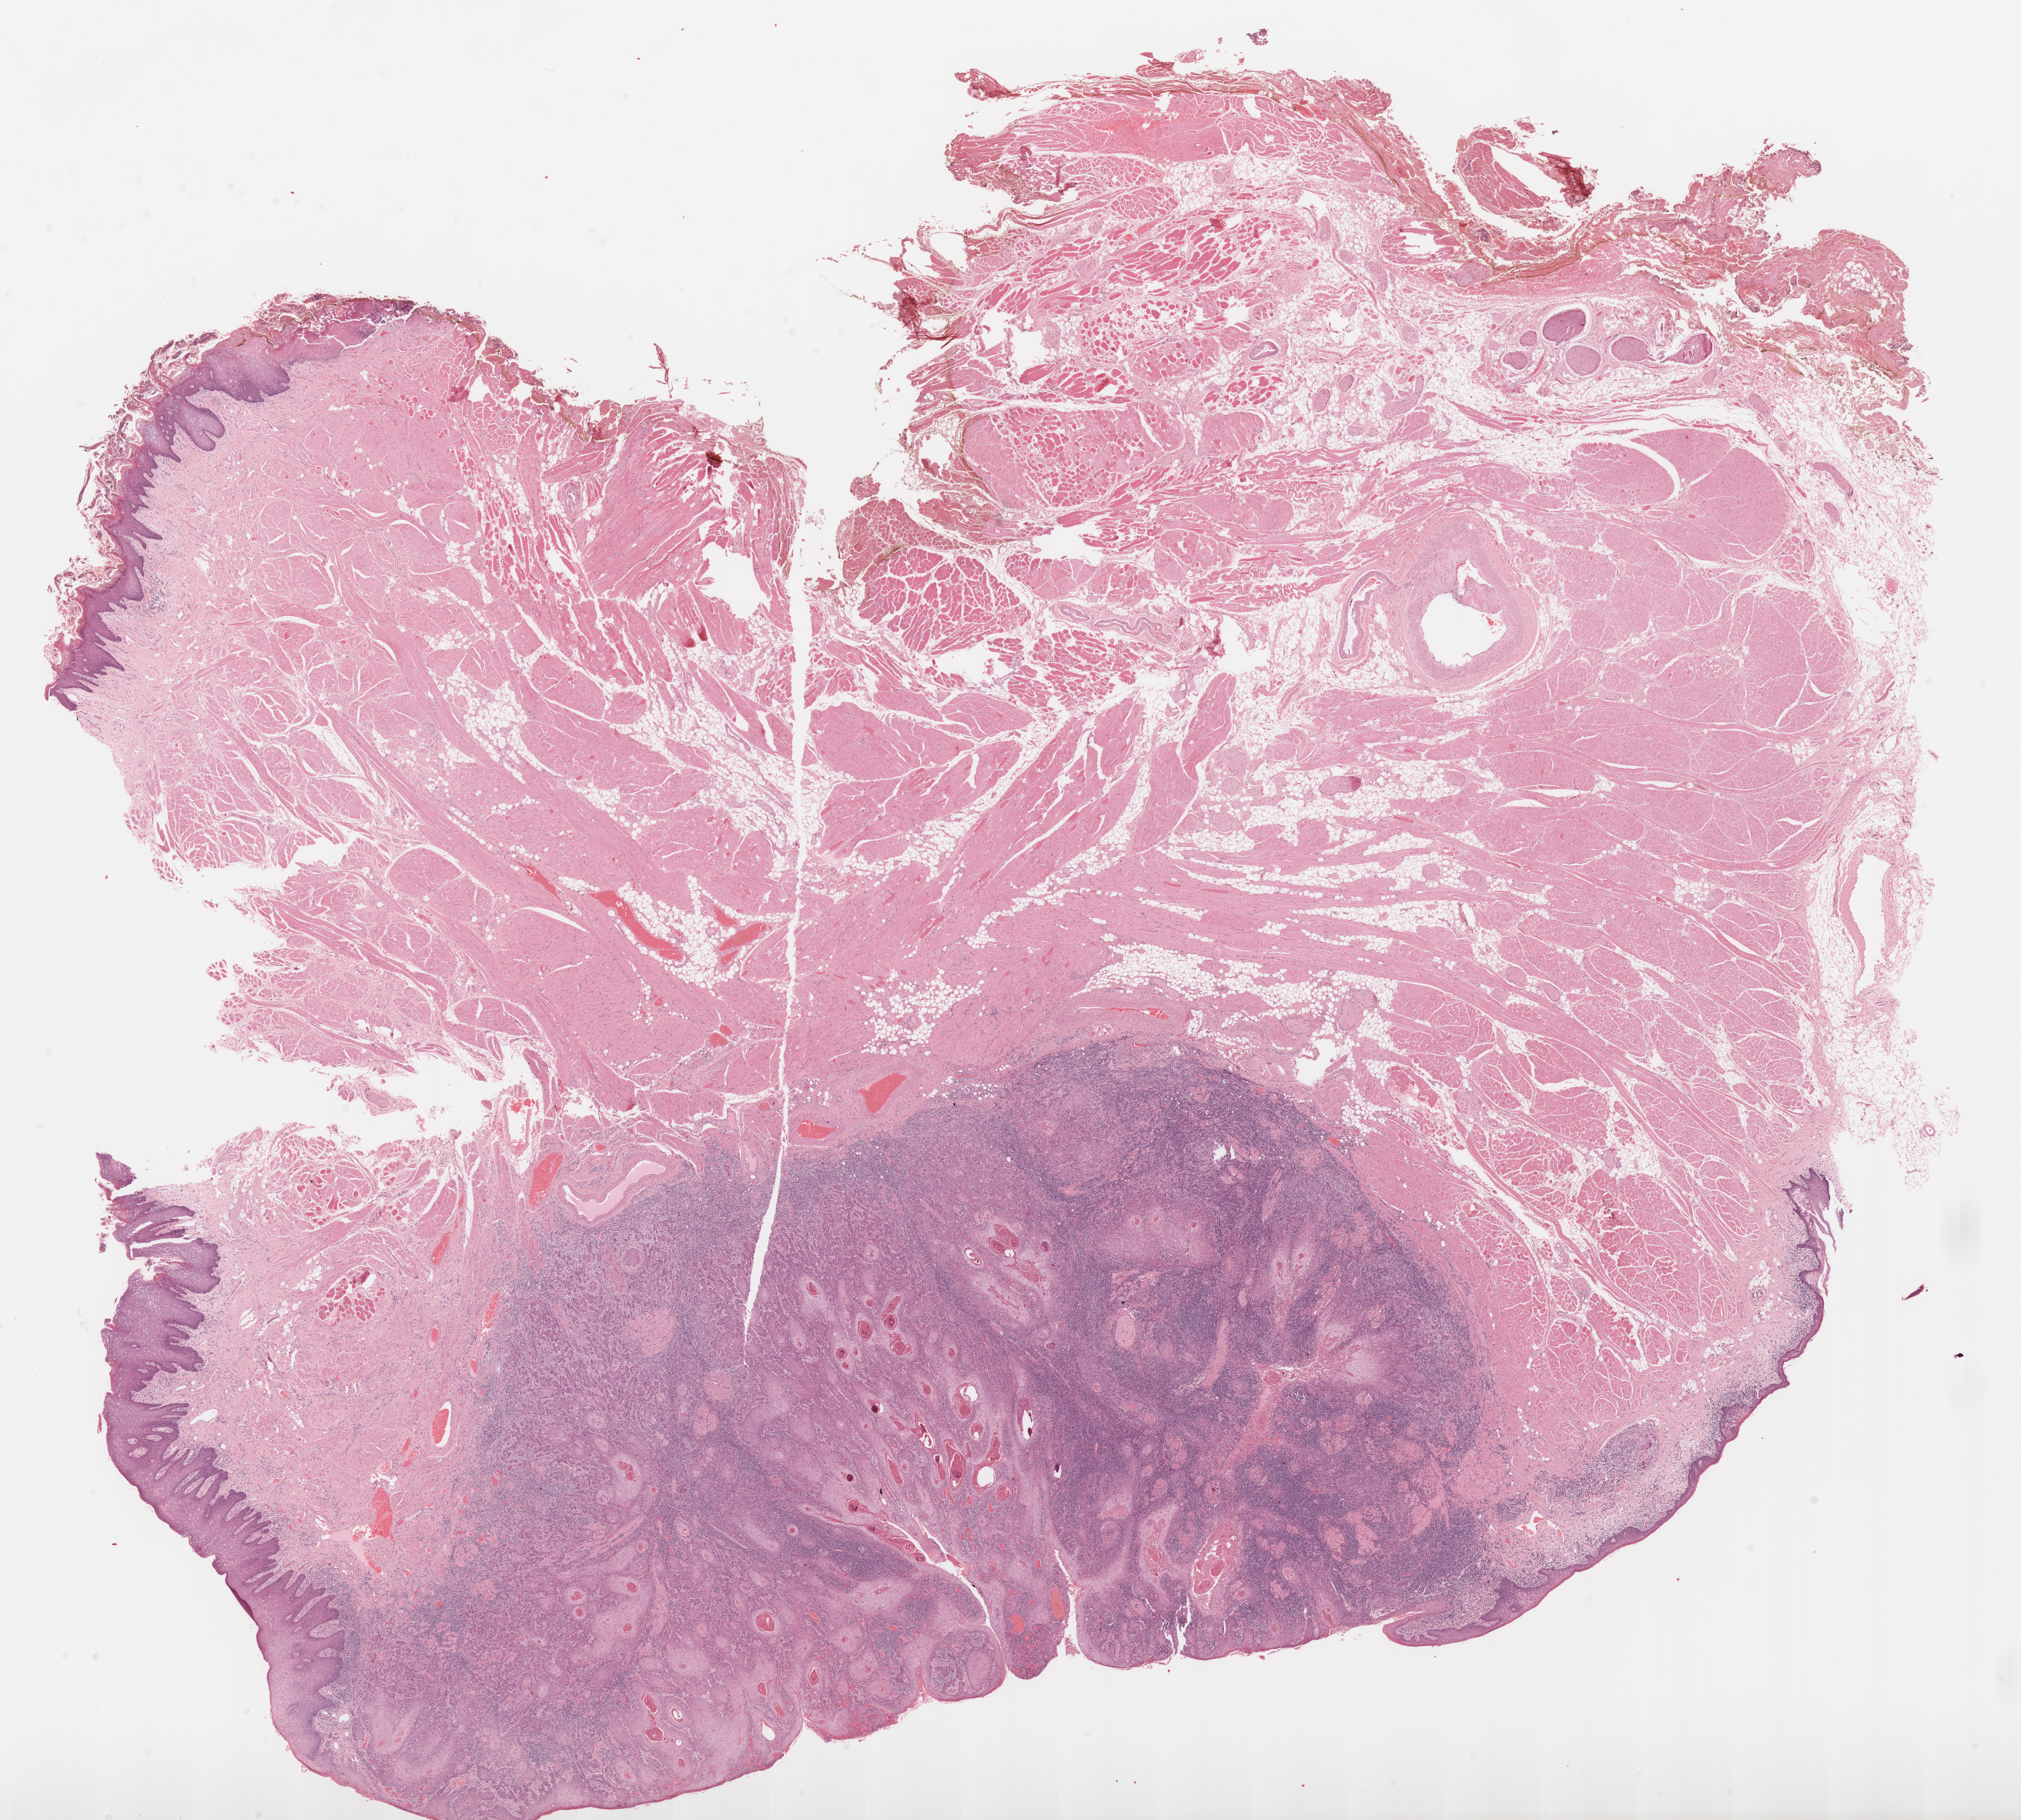
Whole-slide histology image, H&E — whole scanned area (about 21.1 x 19.0 mm) shown as a low-resolution overview, formalin-fixed paraffin-embedded (FFPE) diagnostic section, sample: primary tumour, head and neck. Patient: male, age at initial diagnosis 65 years.
Histologic diagnosis: Squamous cell carcinoma, NOS (tongue, NOS).